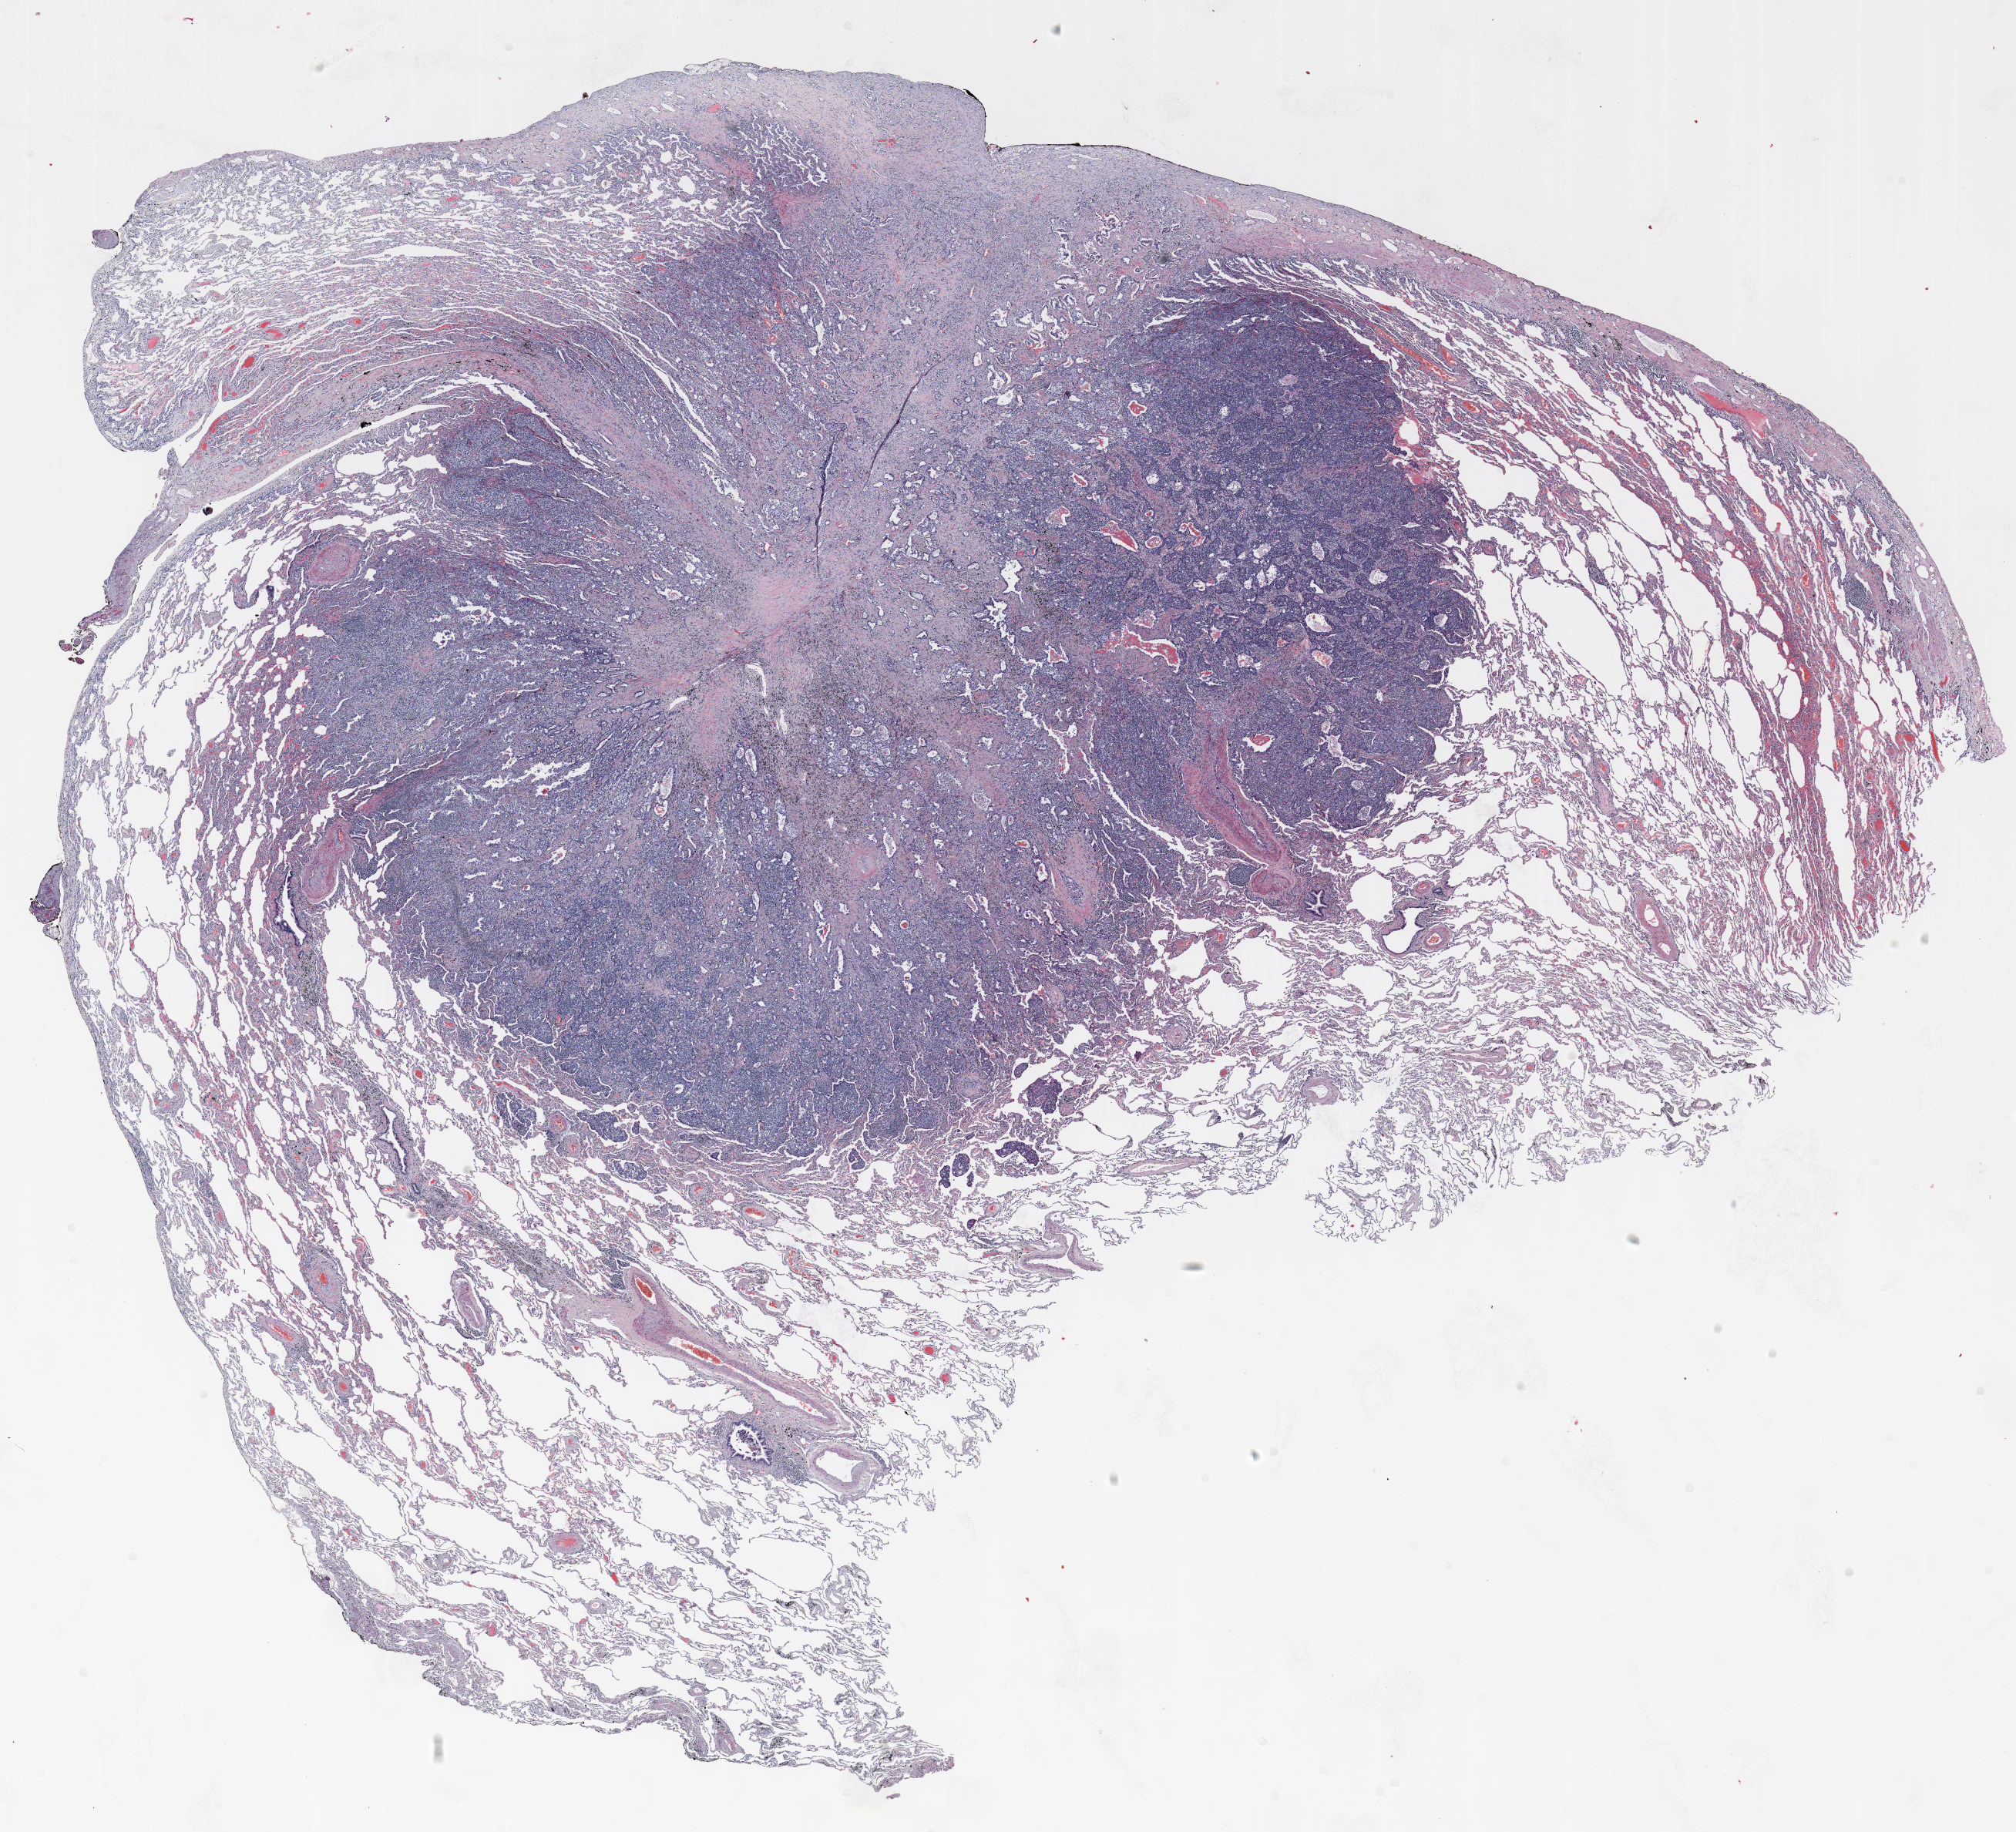
Whole-slide histology image, H&E — shown as a low-resolution overview of the whole scanned area (about 21.0 x 19.1 mm), FFPE section, lung. Female patient, aged 59 at enrolment. Former smoker at enrolment. Grade: moderately differentiated (G2).
- primary tumour location (clinical record): right lower lobe
- ICD-O-3 topography: lower lobe of lung (C34.3)
- participant's lung-cancer diagnosis: Adenocarcinoma, NOS
- tumour size (pathology): 22 mm
- stage (AJCC 6th edition): IIB